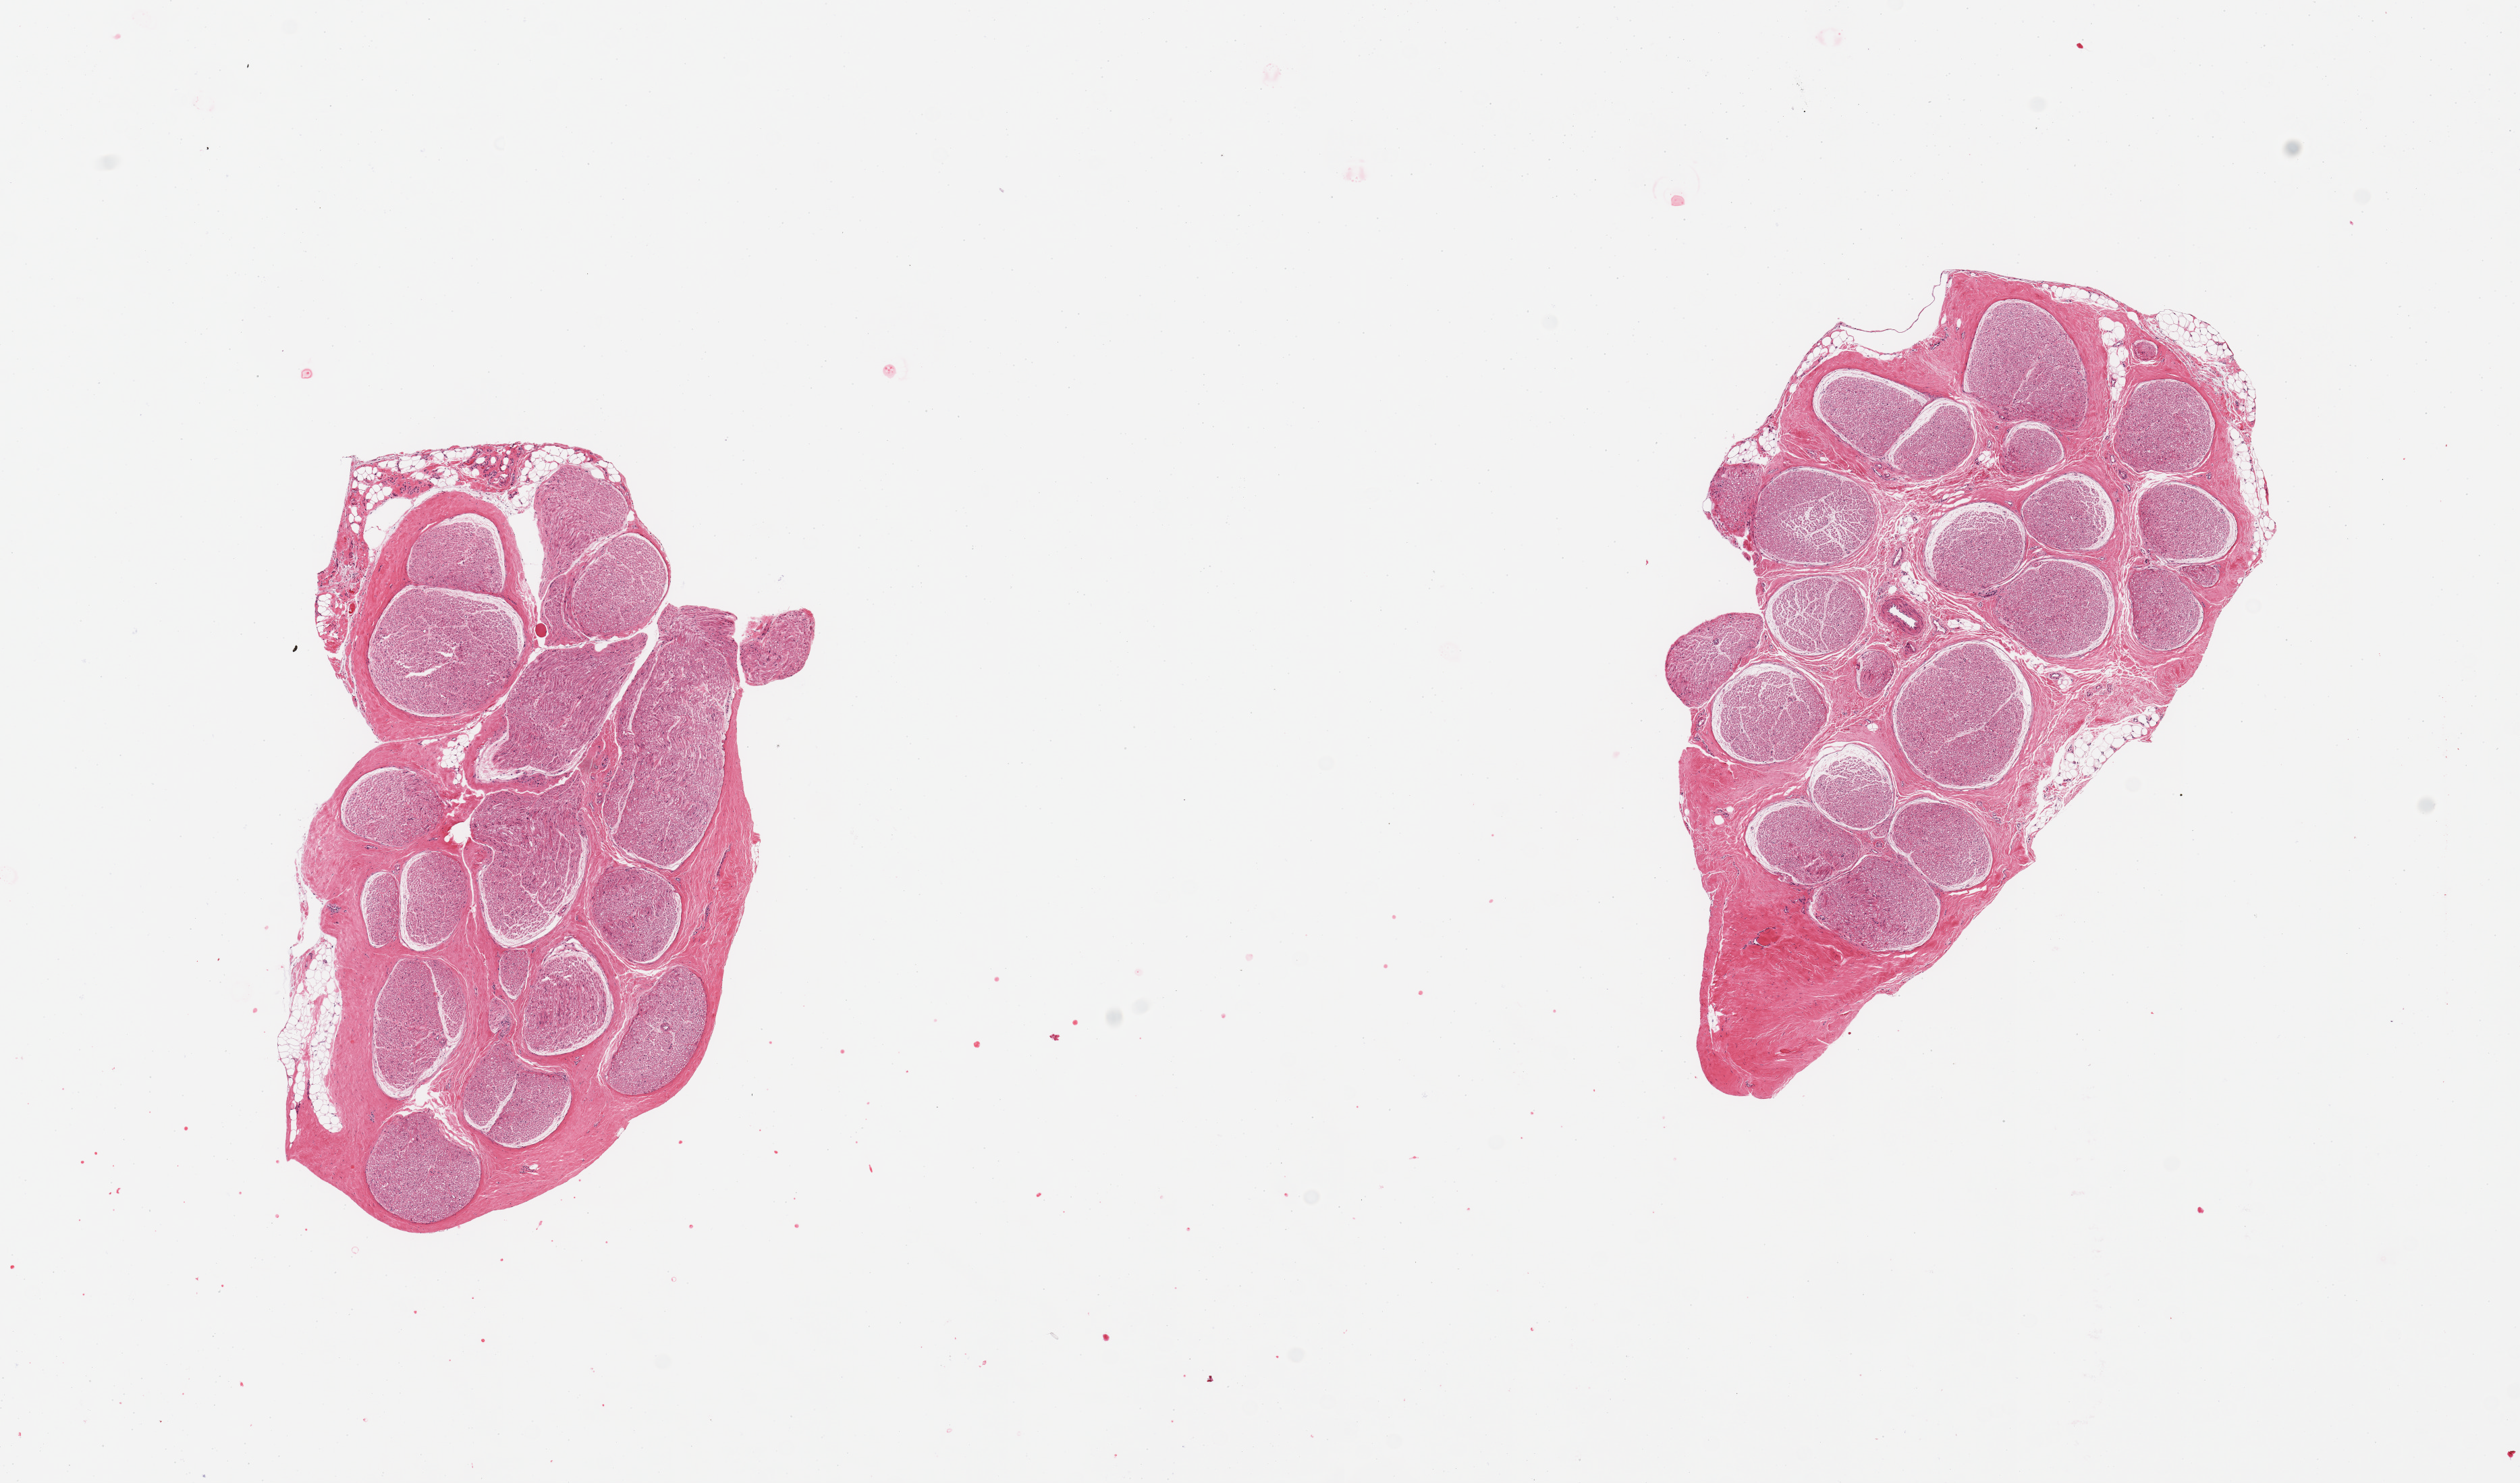
Whole-slide image, haematoxylin and eosin stain, brightfield, shown as a low-resolution overview of the whole scanned area (about 14.8 x 8.7 mm, acquisition: 20x scan). PAXgene-fixed, paraffin-embedded tissue. Target tissue: tibial nerve. Tissue donor sample. Donor: male.
Reviewer comment on this tissue sample: 2 pieces; essentially well trimmed nerve with <10% attached fat.